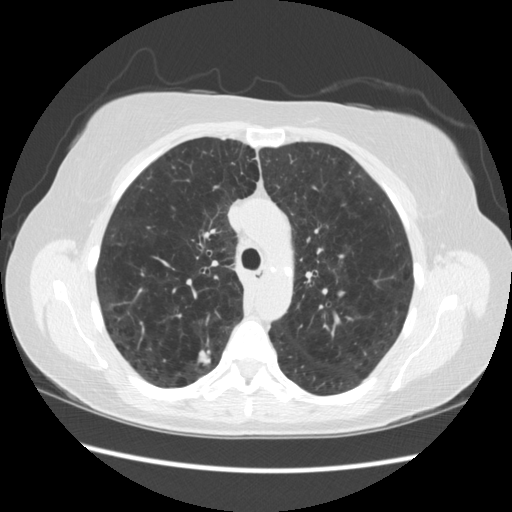
Low-dose screening chest CT, one axial slice. Slice 165 of 235 in the series (ordered by position). Lung window (W 1500 / L -600 HU). 2.5 mm slice thickness. 512 × 512 image matrix, field of view 360 × 360 mm.
Annotated regions visible in this slice (outlined manually by an expert reader):
- lesion 1 (tumor, upper lobe of right lung): bounding box <196,348,212,368> (left, top, right, bottom; pixels)